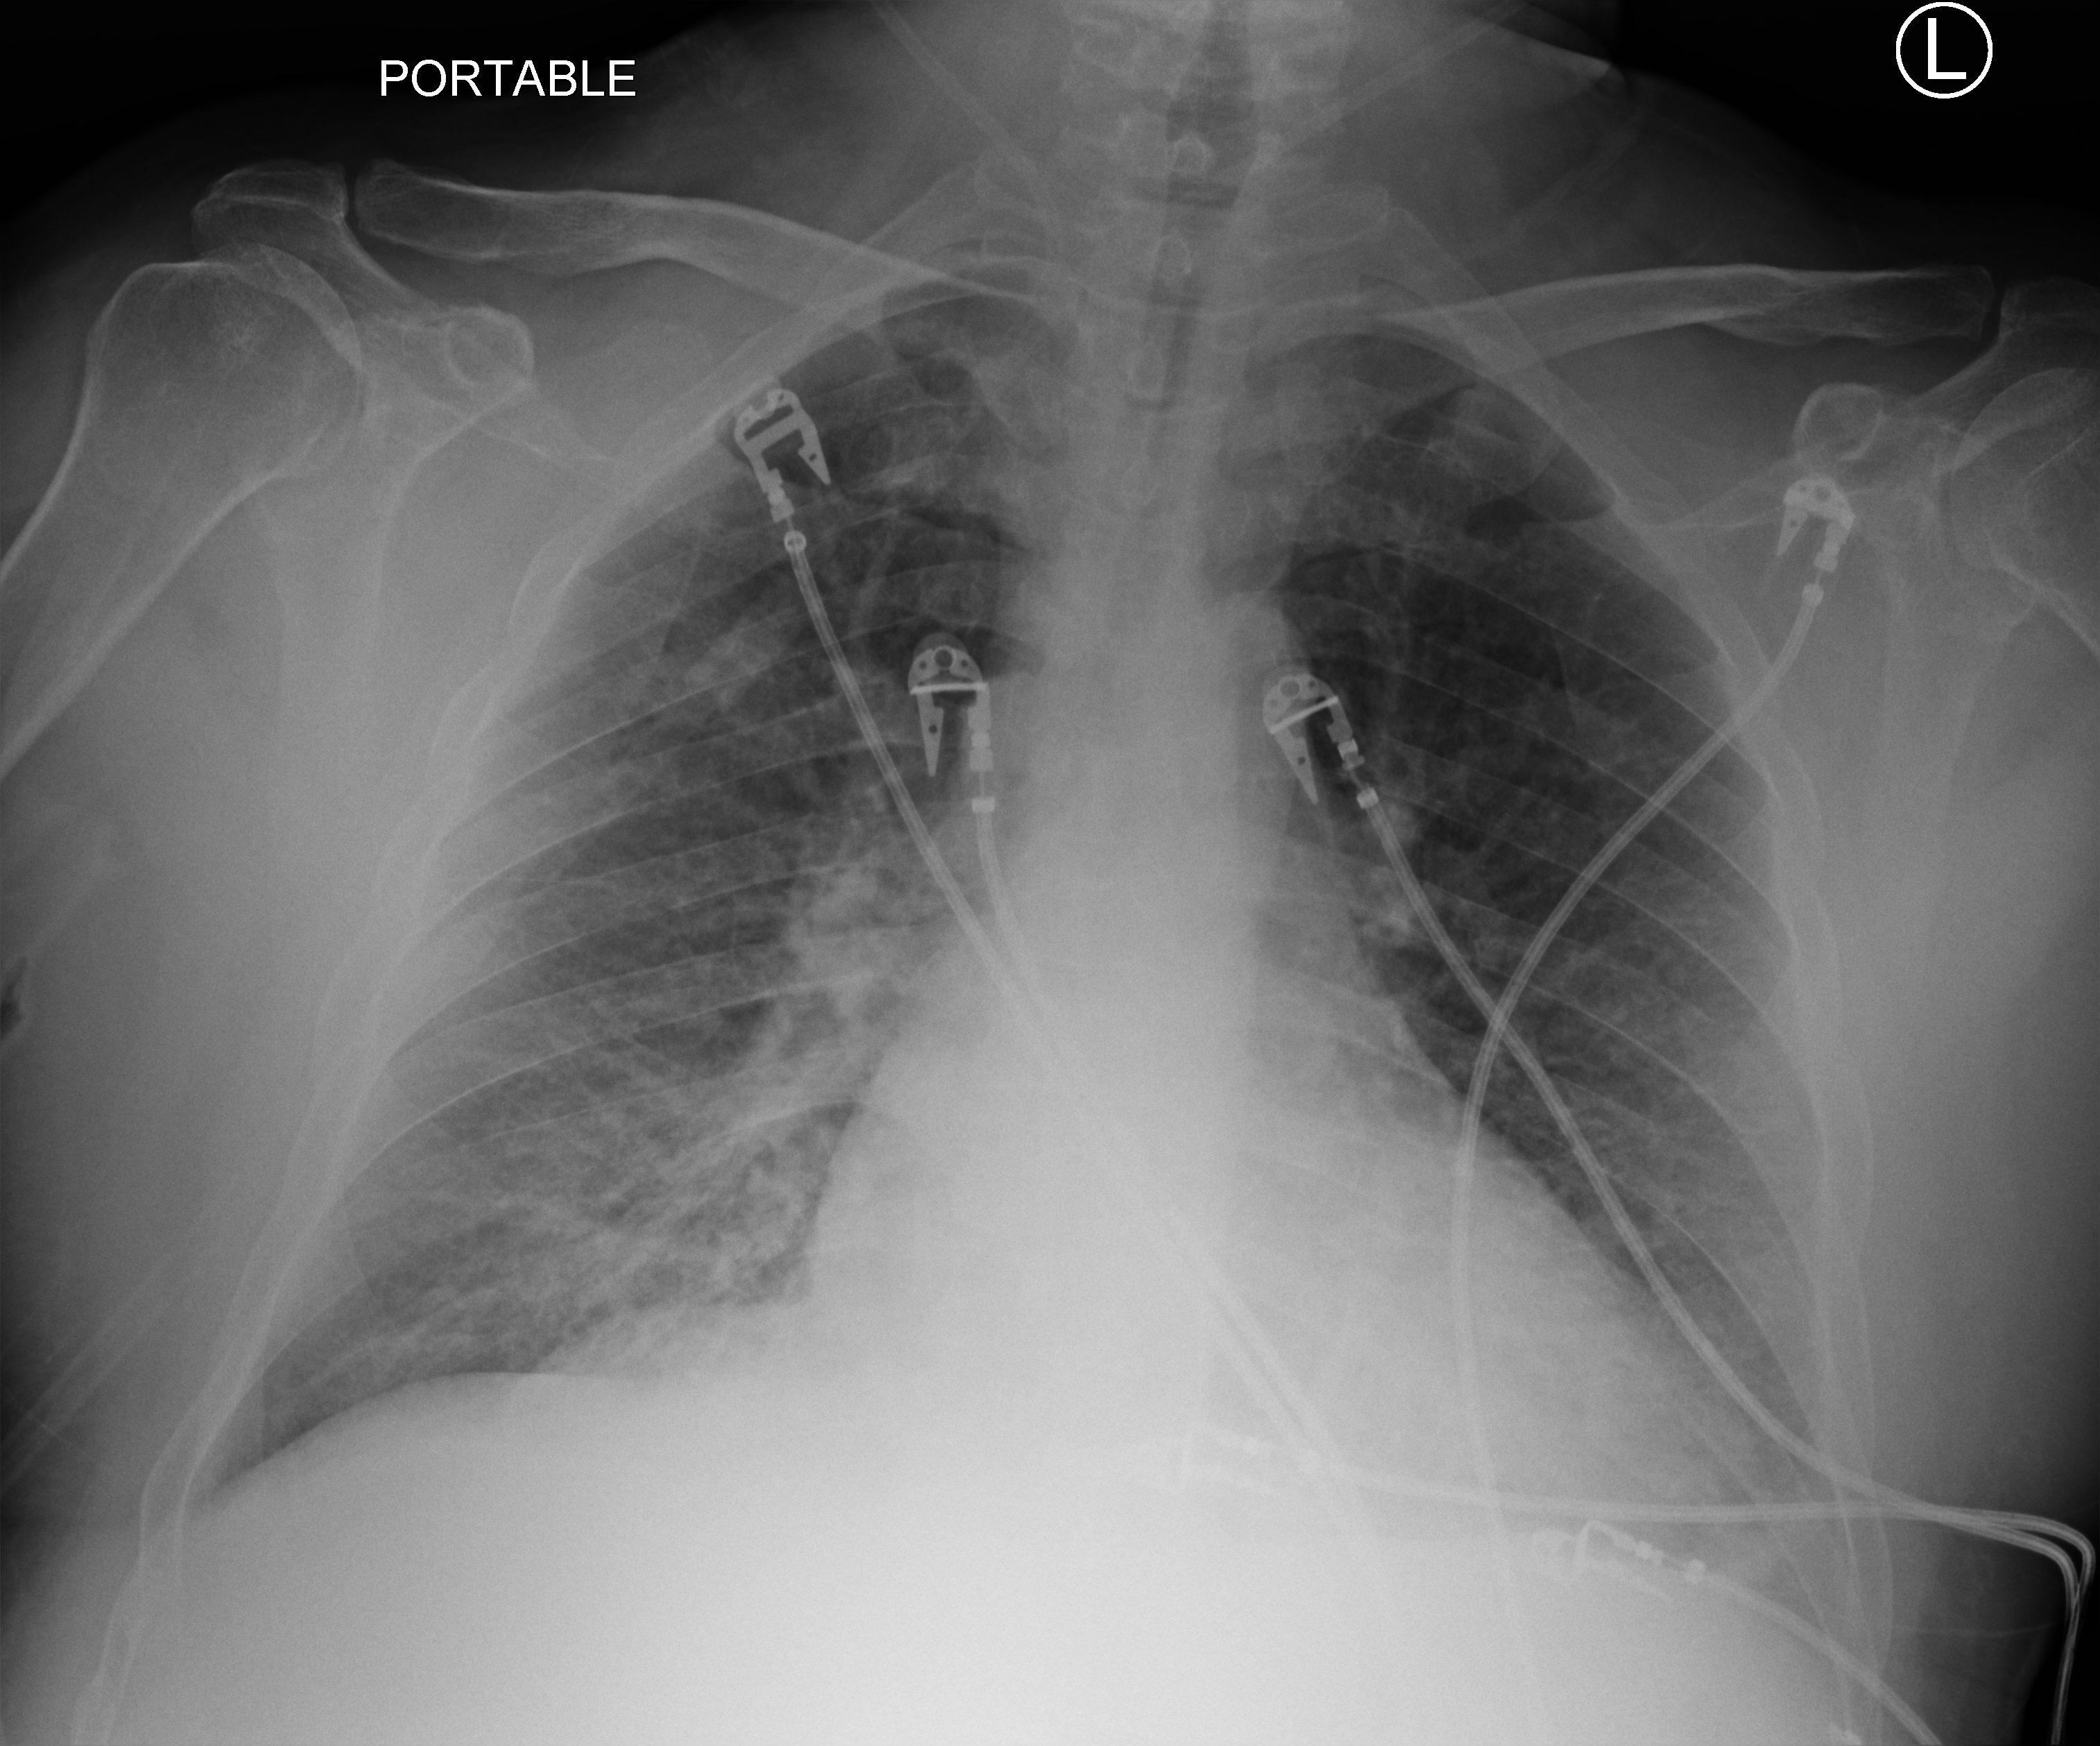
Bedside chest radiograph (computed radiography), anteroposterior (AP) projection. Male patient hospitalised with COVID-19, age 60–74 years.
Hospital-stay facts (about this admission, not read from this image; timing relative to this image not recorded):
- mechanically ventilated during this hospital stay: no
- admitted to intensive care during this hospital stay: no